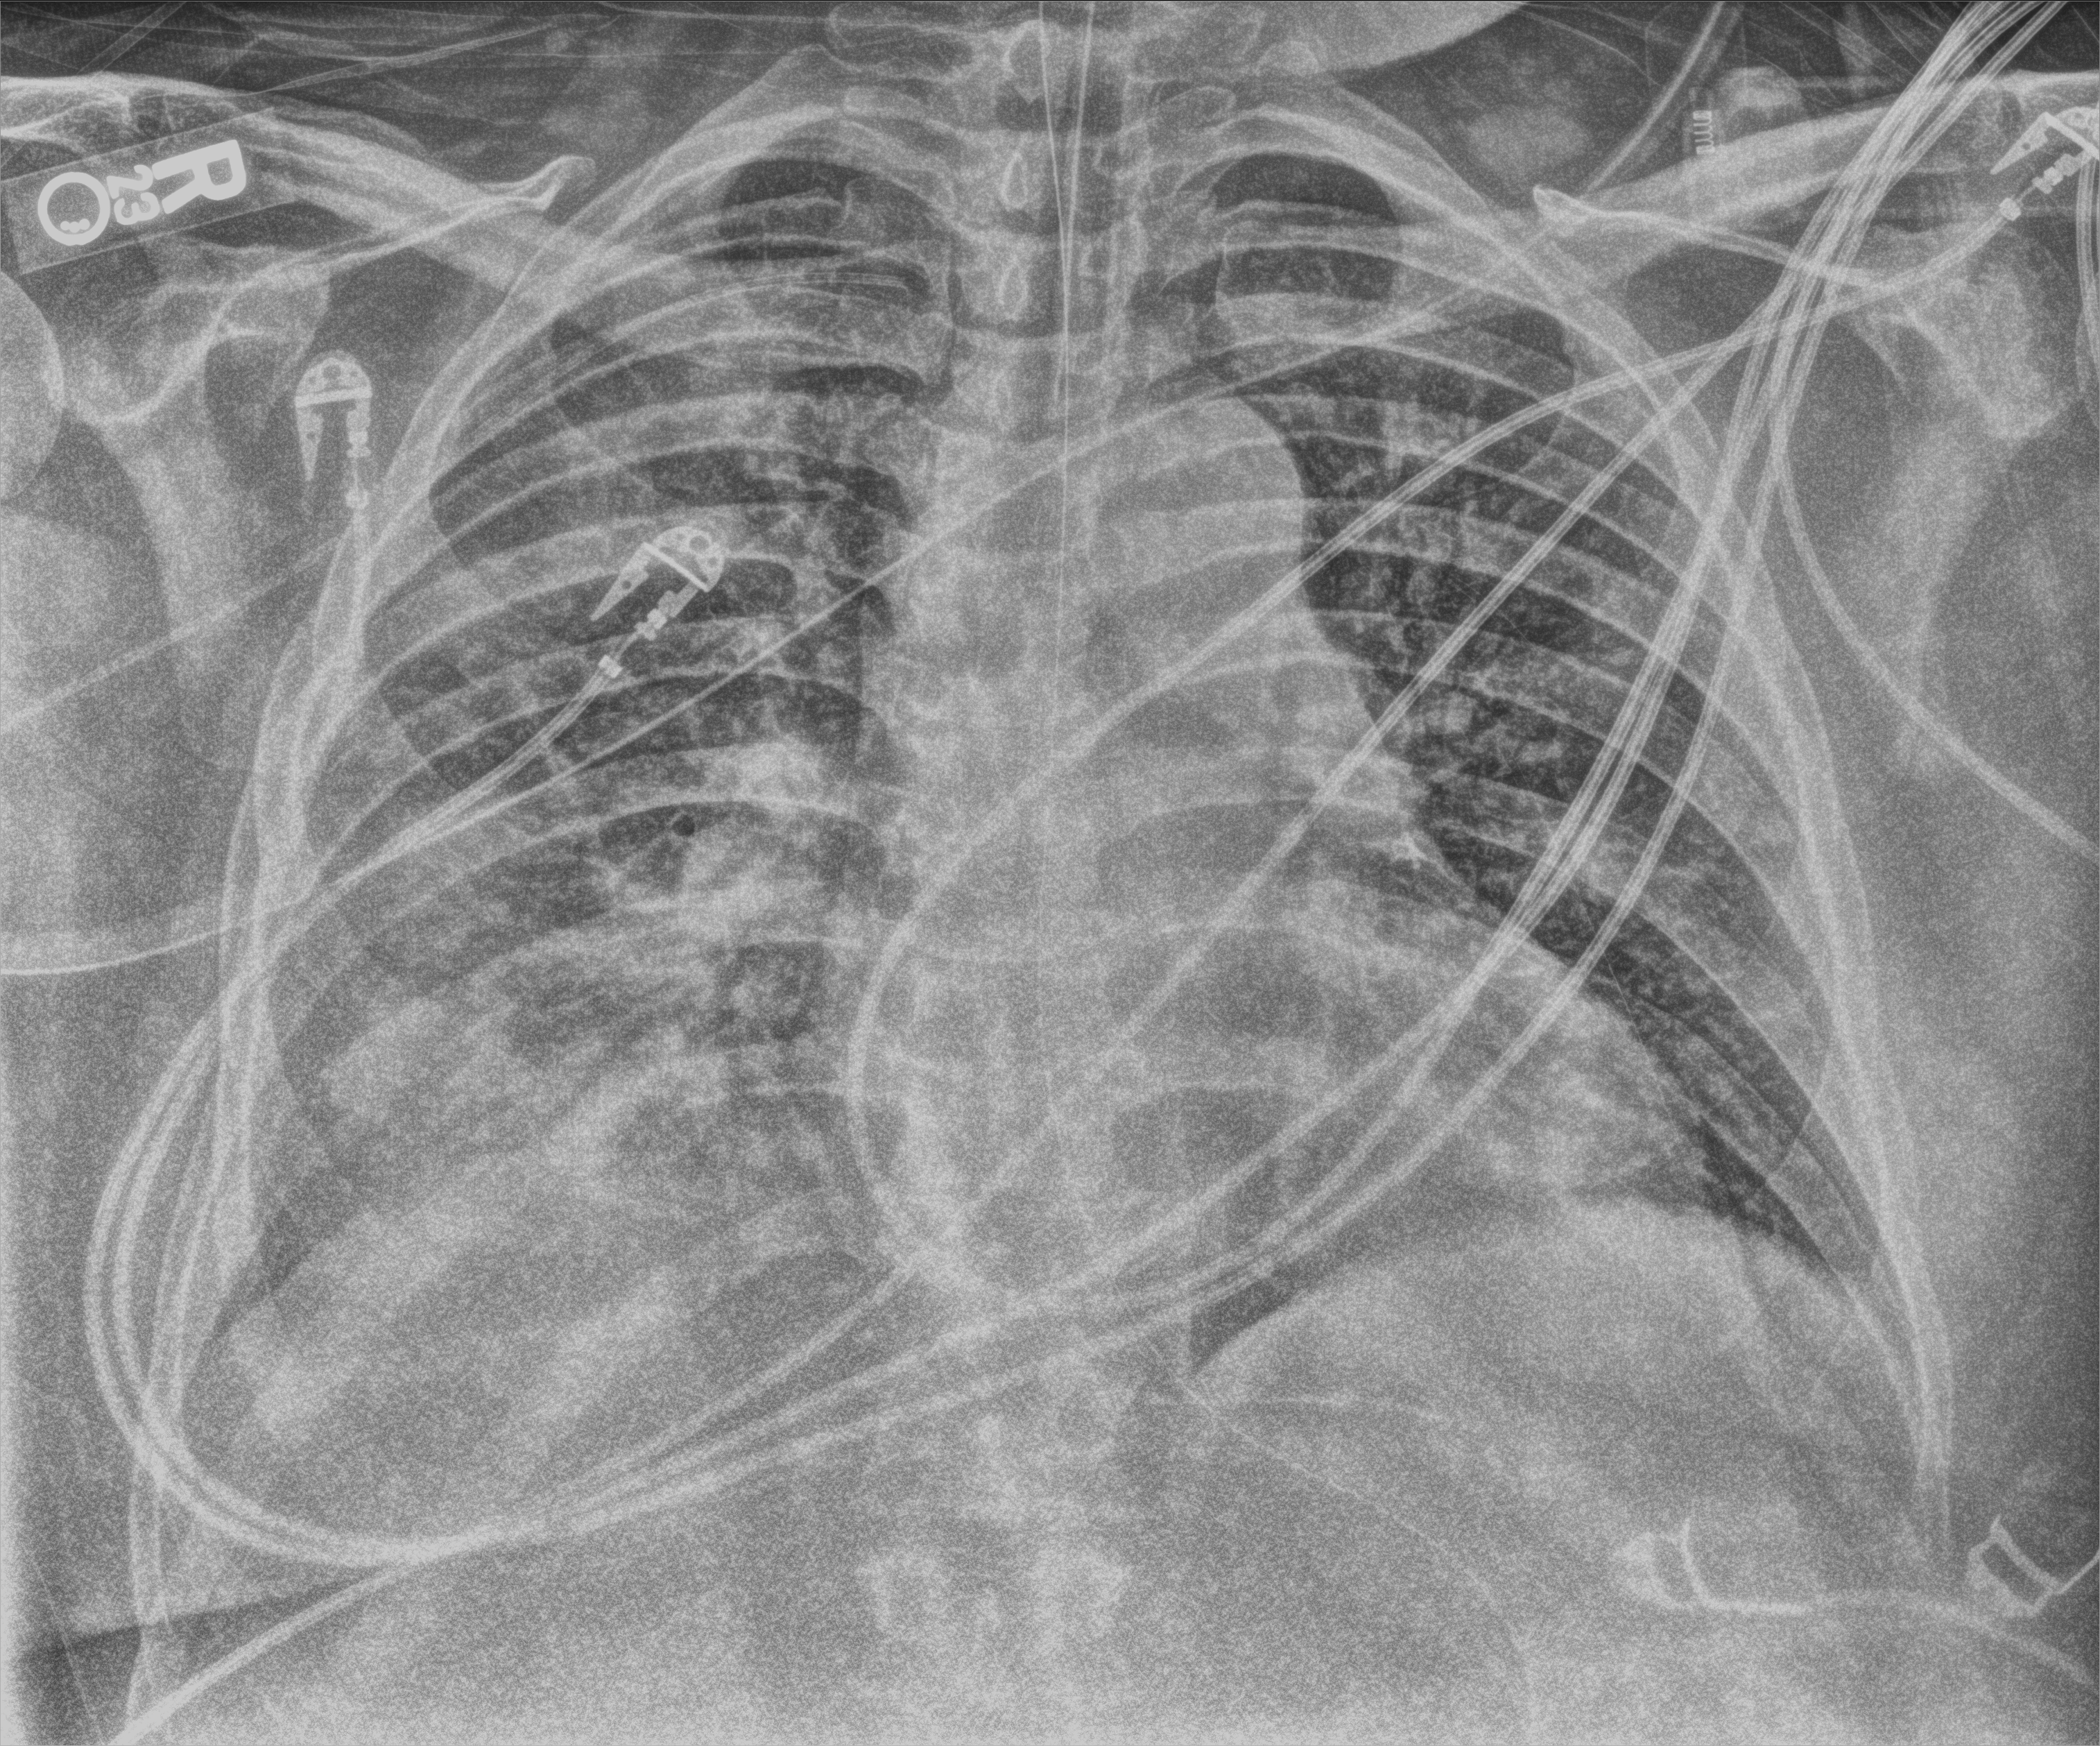
Bedside chest radiograph (computed radiography); anteroposterior (AP) projection. Patient hospitalised with COVID-19; male, aged 18–59 years.
From the hospital-stay record, not from the radiograph (when in the stay this image was taken is not recorded): smoking status (admission record): never; hypertension (admission record): no; admitted to intensive care during this hospital stay: yes.